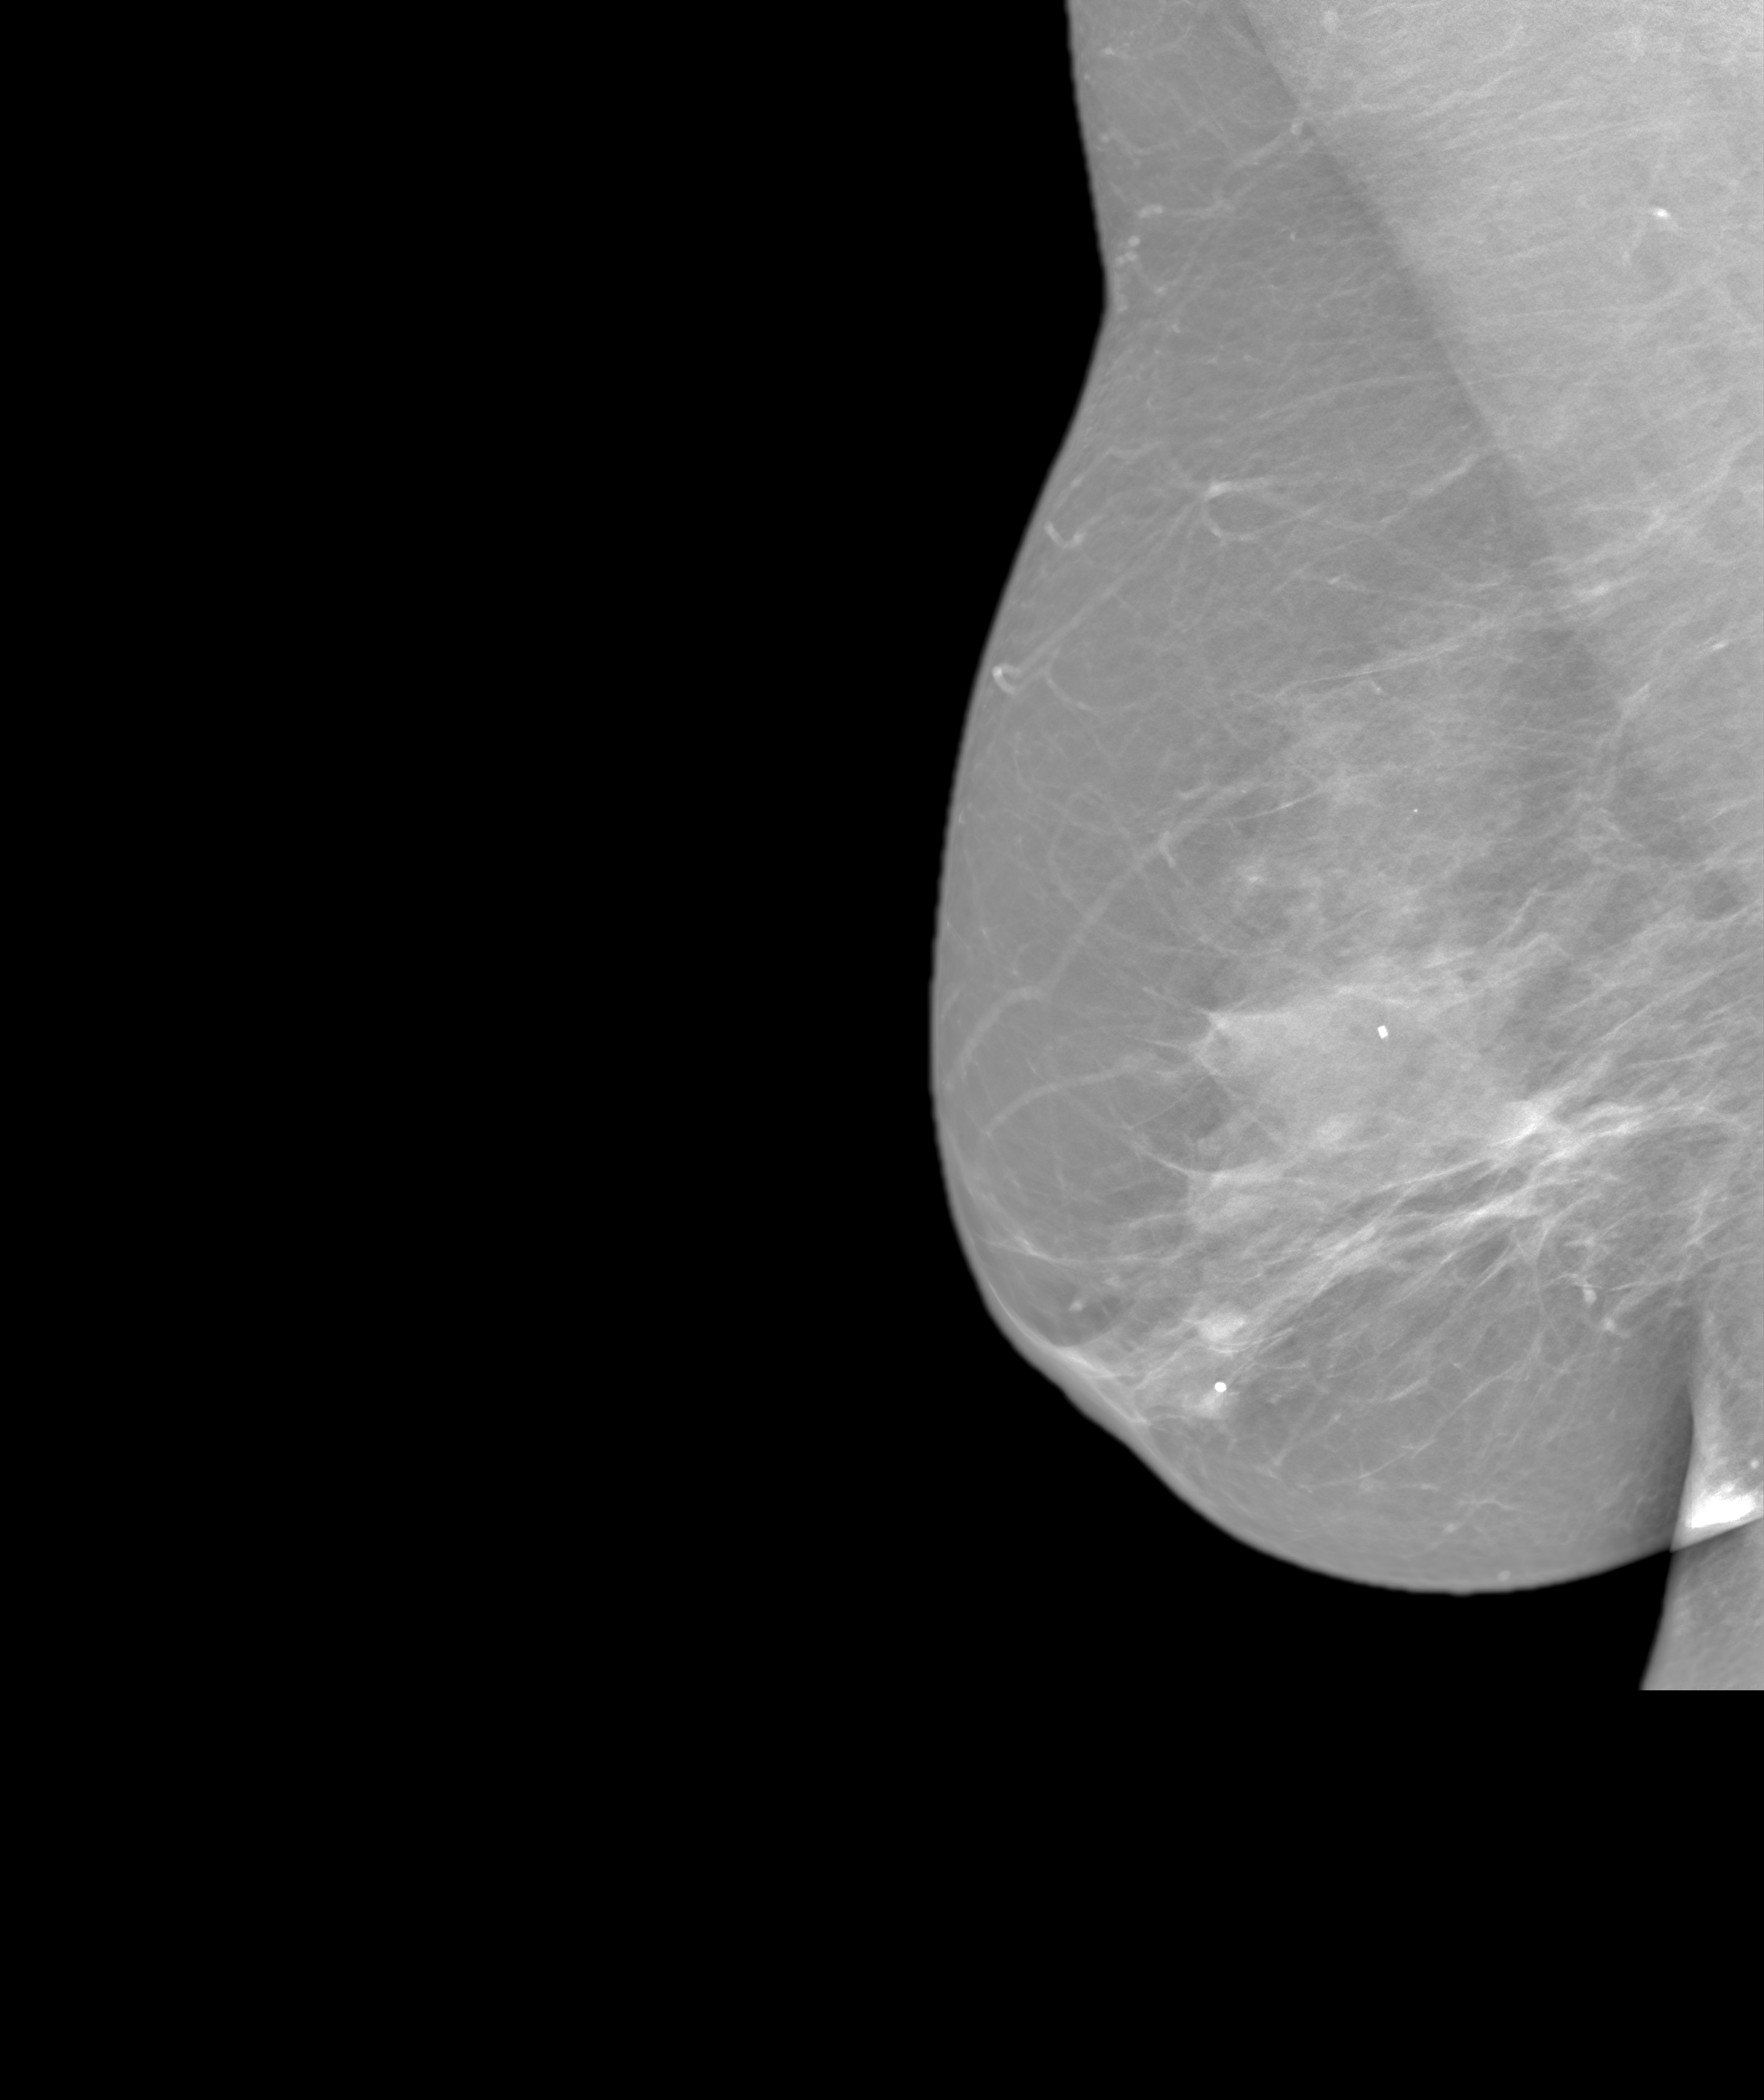
Annual screening mammography examination; system: SenoIris_1SP2(440). Patient aged 48 years (female).
Image type: synthesized 2-D view from tomosynthesis. Breast: right. Projection: mediolateral oblique (MLO) view.